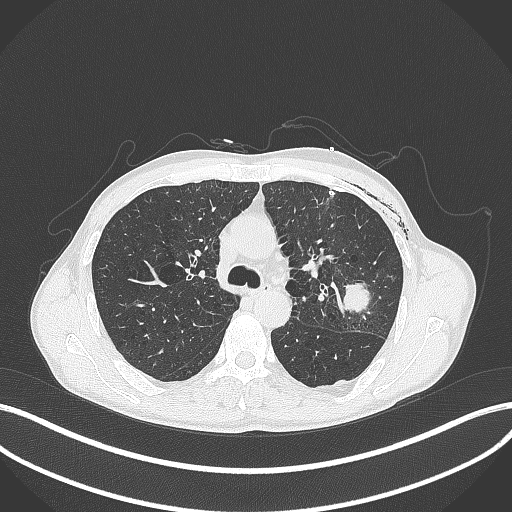
Chest CT, one axial slice; slice 269 of 457 in the series (ordered by position); reconstruction kernel B70f; 120 kVp; lung window (W 1500 / L -600 HU); 1 mm slice thickness; 512 × 512 image matrix, field of view 400 × 400 mm. Male patient, age 58 years. Case-level facts recorded for this patient, not image findings: clinical TNM (as recorded): T3 N0 M0.
Annotated regions visible in this slice (bounding box drawn by a radiologist):
- lung tumour (recorded histology: adenocarcinoma): bounding box <340,278,378,315> (left, top, right, bottom; pixels)